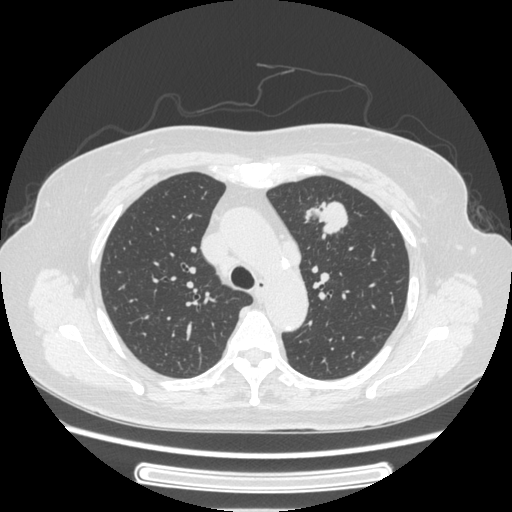
Chest CT, one axial slice. Slice 171 of 227 in the series (ordered by position). Reconstruction kernel STANDARD. 120 kVp. Lung window (W 1500 / L -600 HU). 512 × 512 image matrix, field of view 363 × 363 mm. Patient: female, 77 years. From the clinical record (not read from this slice): clinical TNM (as recorded): T1c N3 M0.
Annotated regions visible in this slice (bounding box drawn by a radiologist):
- lung tumour (recorded histology: adenocarcinoma): bounding box (x1, y1, x2, y2) in pixels: (300, 189, 348, 239)